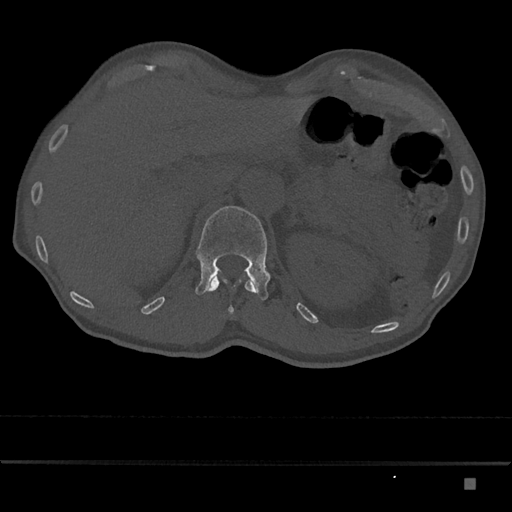
CT including the spine, one axial slice. Slice 570 of 797 in the series (ordered by position). Reconstruction kernel Br40s/3. 120 kVp. Bone window (W 1800 / L 400 HU). 0.5 mm slice thickness. 512 × 512 image matrix, field of view 390 × 390 mm. Patient: male, 72 years. From the clinical record (not read from this slice): primary cancer: prostate.
Annotated regions visible in this slice (semi-automatic segmentation, software-assisted and operator-edited):
- L1 vertebra: box from (x=195, y=206) to (x=270, y=301) px
- T12 vertebra: (x=206, y=276)–(x=256, y=314)